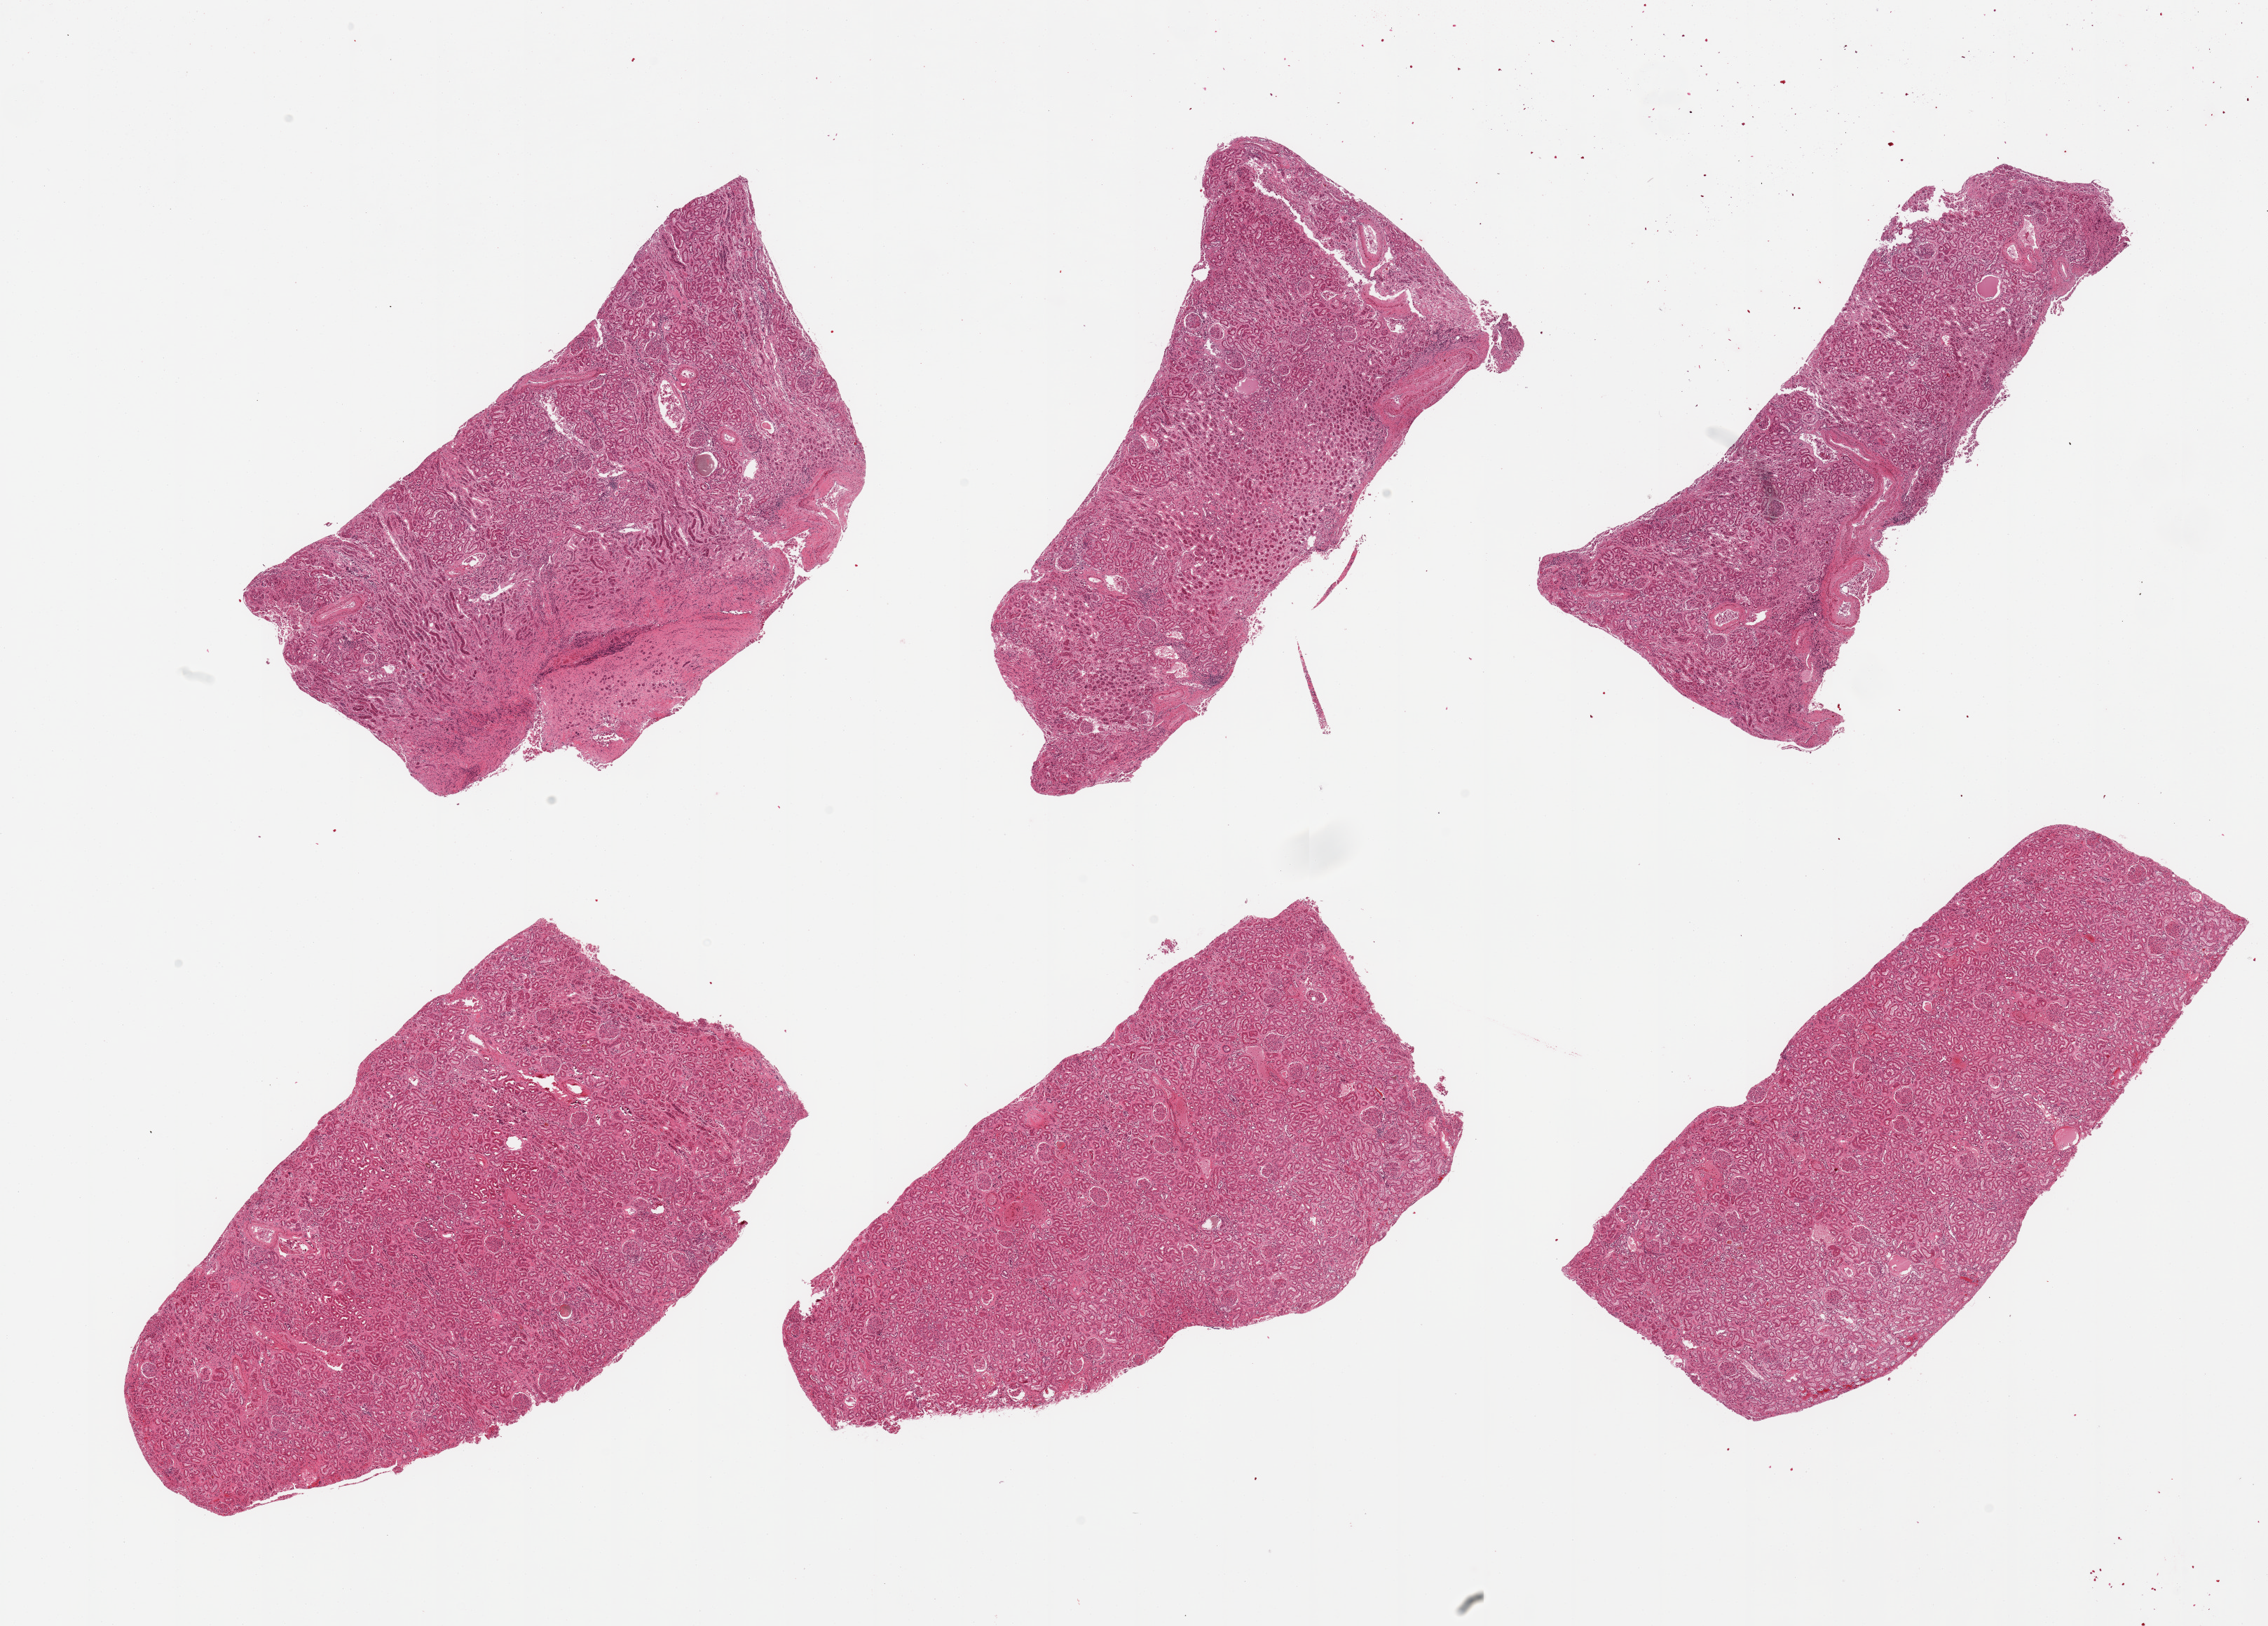
Whole-slide image, haematoxylin and eosin stain, a low-resolution overview of the entire scanned area, about 25.6 x 18.4 mm; PAXgene-fixed paraffin-embedded (PFPE) section; sampled site (target tissue): renal cortex; tissue donor sample. Donor: male.
- pathologist's review note for this sample: 6 pieces; glomeruli in all sections